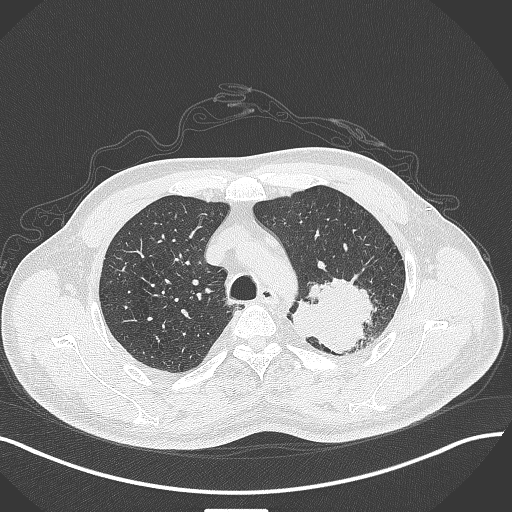
Chest CT, one axial slice. Position 327 of 429 along the scan axis. Reconstruction kernel B70f. 120 kVp. Lung window (W 1500 / L -600 HU). 1 mm slice thickness. 512 × 512 image matrix, field of view 400 × 400 mm. Male patient, age 55 years. From the clinical record (not read from this slice): clinical TNM (as recorded): T3 N0 M1c.
Structures marked on this image (bounding box drawn by a radiologist):
- lung tumour (recorded histology: adenocarcinoma): bounding box <294,271,378,358> (left, top, right, bottom; pixels)